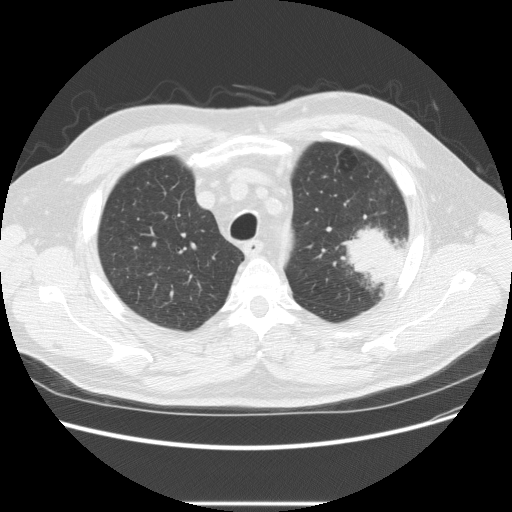
Axial slice from a low-dose chest CT screening exam; first (baseline) screen; lung window (W 1500 / L -600 HU); 2.5 mm slice thickness; 120 kVp. Male participant, aged 73 years at enrolment. Former smoker at enrolment.
• Expert-annotated lung lesion, bounding box <332,216,412,285> (left, top, right, bottom; pixels).
• The screening reader recorded 2 non-calcified nodules or masses ≥4 mm on this exam; which of them this box marks is not recorded.
• Official screen result: positive, change unspecified: nodule(s) >= 4 mm or enlarging nodule(s), mass(es), or other non-specific abnormalities suspicious for lung cancer.
• Participant outcome: lung cancer diagnosed 11 days after this screen — bronchiolo-alveolar adenocarcinoma, NOS, other location, well differentiated (G1), stage IV (AJCC 6th edition).